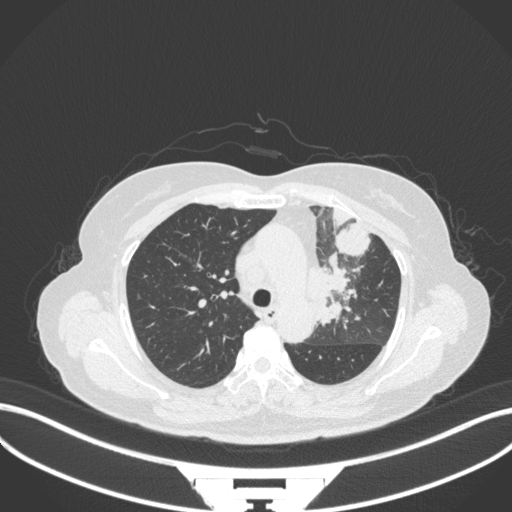
Chest CT, one axial slice; position 236 of 382 along the scan axis; 120 kVp; lung window (W 1500 / L -600 HU); 512 × 512 image matrix, field of view 400 × 400 mm. Patient: female, 64 years. Case-level facts recorded for this patient, not image findings: clinical TNM (as recorded): T2a N2 M0.
Annotated regions visible in this slice (rectangle marked by the reading radiologist):
- lung tumour (recorded histology: adenocarcinoma): box from (x=305, y=257) to (x=359, y=332) px
- lung tumour (recorded histology: adenocarcinoma): (x=333, y=218)–(x=374, y=259)